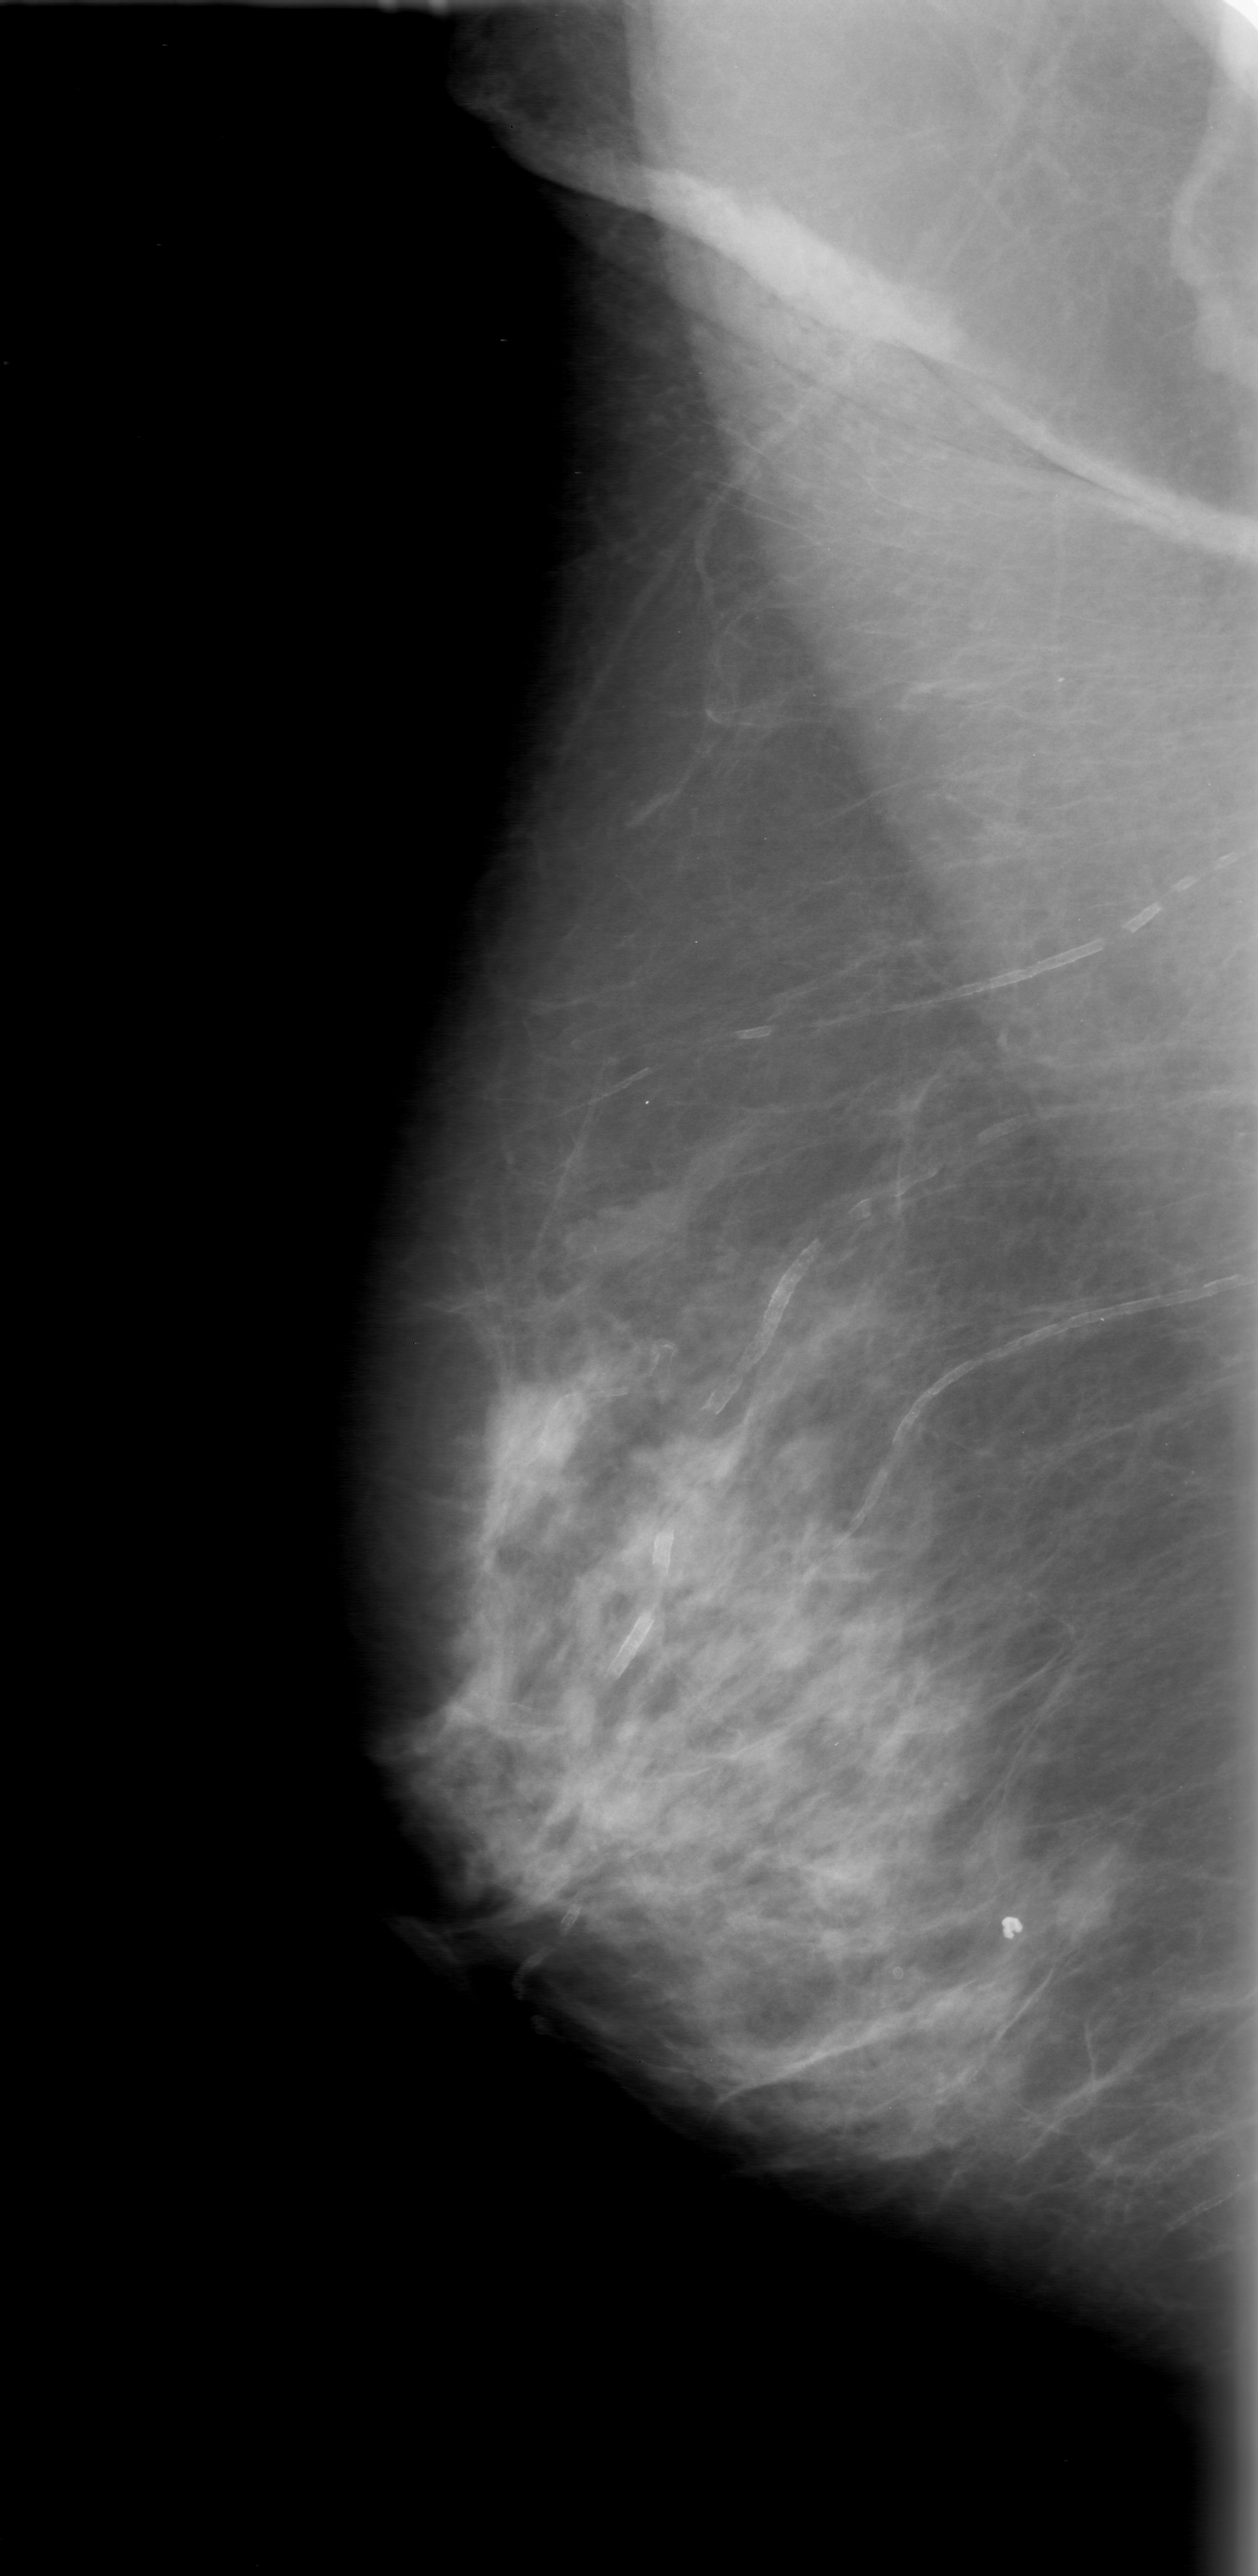
Scanned film-screen mammogram; right breast; MLO view; breast composition: scattered fibroglandular densities (BI-RADS density category 2 of 4); 1258 × 2576 image matrix.
Expert-marked regions of interest on this image (one box per marked abnormality):
- mass, shape round, margins obscured; BI-RADS assessment category 0; subtlety rating 4 on a 1 (subtle) to 5 (obvious) scale; pathology (as recorded): benign: box from (x=457, y=1356) to (x=611, y=1507) px